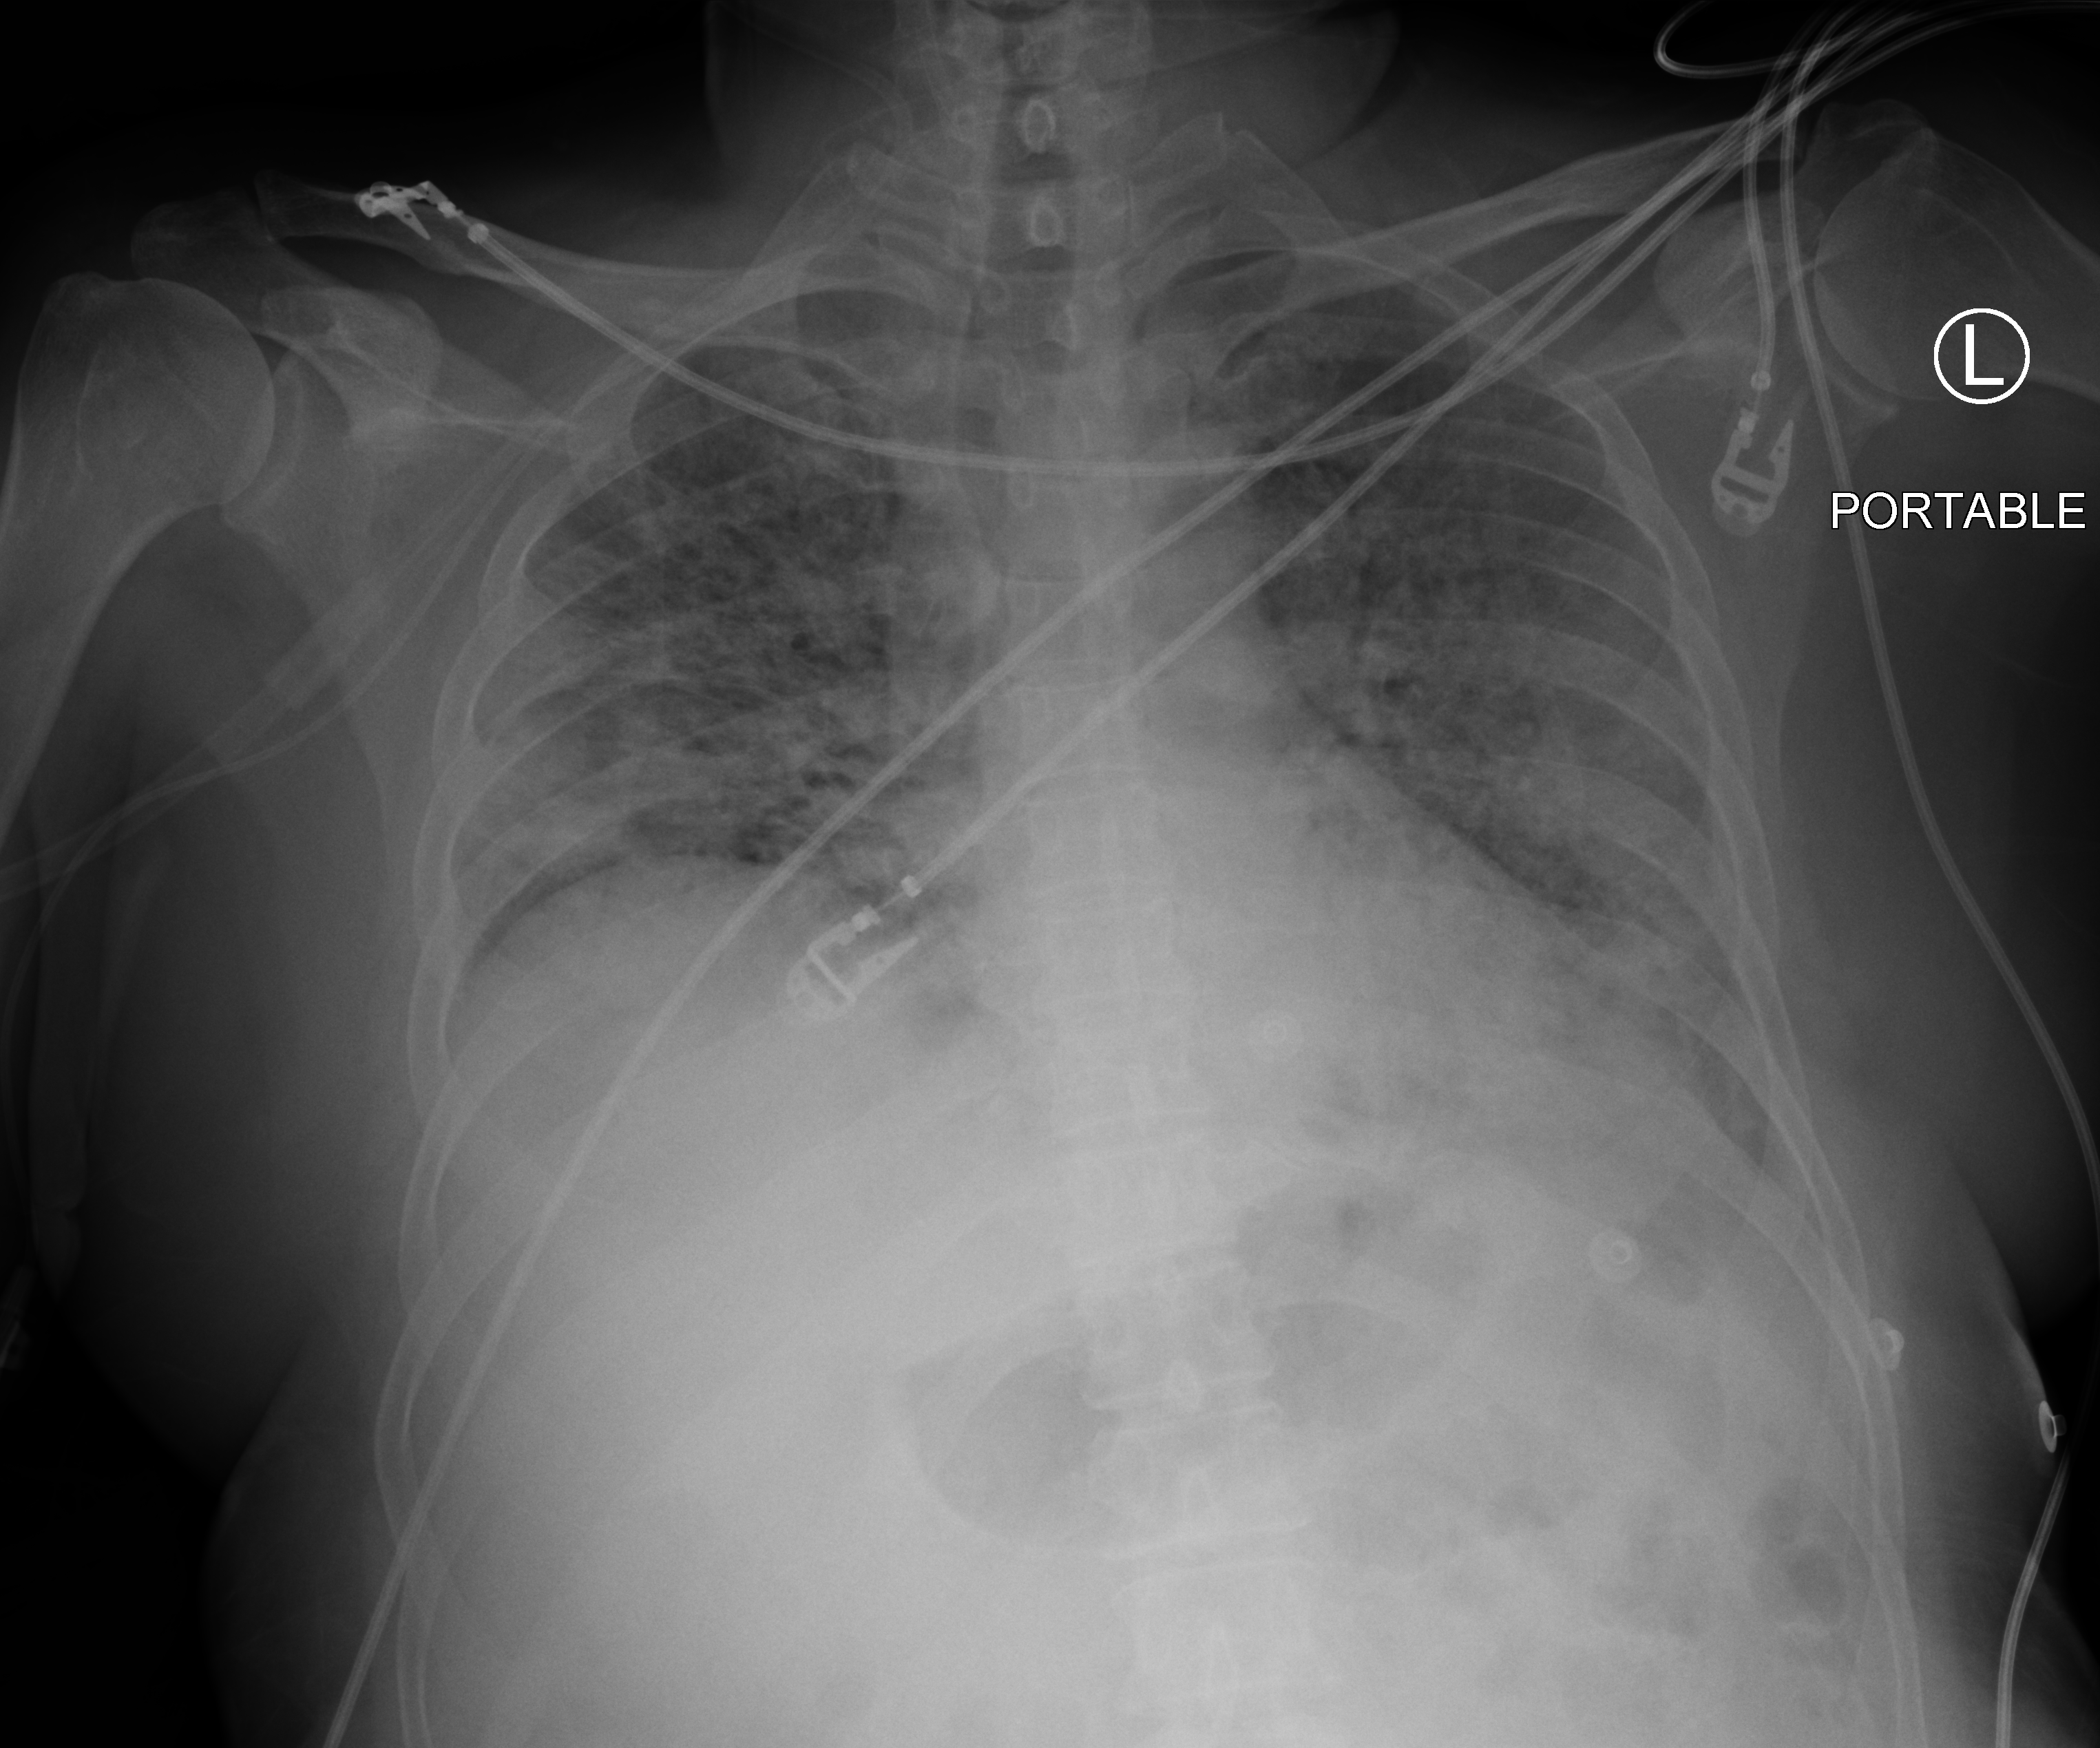
Bedside chest radiograph (computed radiography). Male patient hospitalised with COVID-19, age 18–59 years.
Hospital-stay facts (about this admission, not read from this image; timing relative to this image not recorded):
- mechanically ventilated during this hospital stay: yes
- admitted to intensive care during this hospital stay: yes
- chronic kidney disease (admission record): no